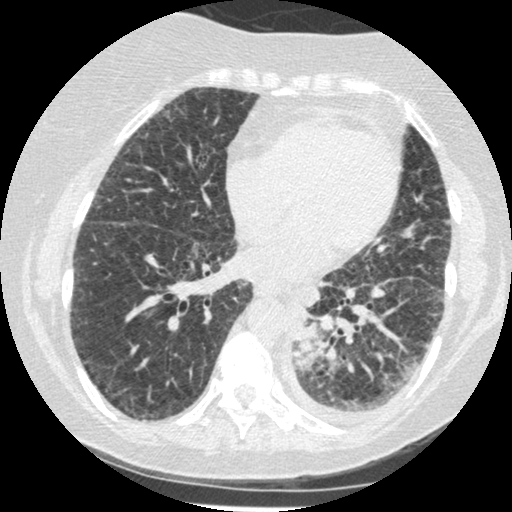
Chest CT (low-dose screening protocol), one axial image. Third annual screen. Lung window (W 1500 / L -600 HU). 1.25 mm slice thickness. Standard (soft-tissue) reconstruction kernel (STANDARD). 120 kVp. Slice 262 of 341 in the series. Female participant, aged 60 years at enrolment.
Expert-annotated lung lesion, bounding box <279,301,344,377> (left, top, right, bottom; pixels). Screening reader's record for this exam (one nodule recorded; not confirmed to be the boxed lesion): non-calcified nodule or mass ≥4 mm, left lower lobe, 54 × 38 mm, smooth margins, soft tissue attenuation, pre-existing on the prior screen: yes; interval growth: yes. Participant outcome: lung cancer diagnosed 15 days after this screen — small cell carcinoma, NOS, left lower lobe, undifferentiated (G4), stage IV (AJCC 6th edition), 69 mm at pathology.